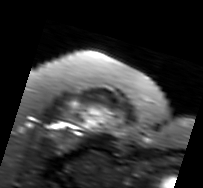
MRI of an extremity soft-tissue mass, one axial slice. Position 64 of 91 along the scan axis. T2-weighted fat-saturated. MR volume resampled by the dataset authors to the PET/CT grid (not the native acquisition matrix). 3.27 mm slice thickness. 203 × 188 image matrix, field of view 198 × 184 mm. Female patient. Case-level facts recorded for this patient, not image findings: histological type: malignant solitary fibrous tumor; grade: intermediate; site of the primary tumour: right thigh.
Structures marked on this image (expert contour drawn on MRI and transferred to this co-registered scan by the dataset authors):
- gross tumour volume including surrounding oedema: box from (x=56, y=101) to (x=125, y=148) px
- gross tumour volume (mass): (x=83, y=106)–(x=100, y=127)